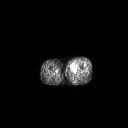
FDG PET of an extremity soft-tissue mass (from a PET/CT study), one axial slice. Position 228 of 267 along the scan axis. 128 × 128 image matrix, field of view 700 × 700 mm. Patient: male, 48 years. Case-level facts recorded for this patient, not image findings: histological type: pleiomorphic leiomyosarcoma; grade: high; site of the primary tumour: left thigh.
Structures marked on this image (expert contour drawn on MRI and transferred to this co-registered scan by the dataset authors):
- gross tumour volume including surrounding oedema: box from (x=69, y=64) to (x=76, y=71) px
- gross tumour volume (mass): (x=70, y=65)–(x=75, y=71)